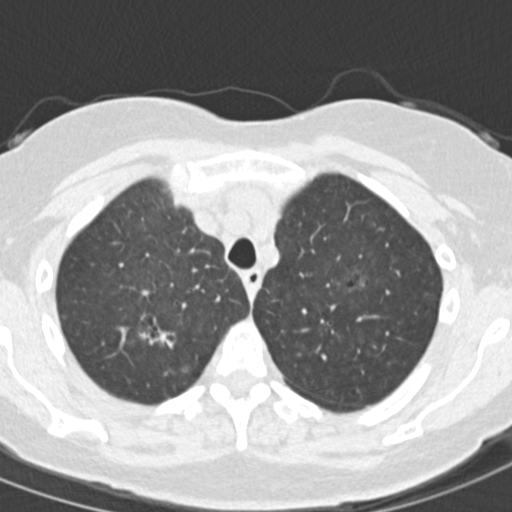
Low-dose screening chest CT, one axial slice. Slice 123 of 157 in the series (ordered by position). 120 kVp. Lung window (W 1500 / L -600 HU). 512 × 512 image matrix, field of view 280 × 280 mm.
Outlined on this slice (manually delineated by an expert):
- lesion 1 (tumor, upper lobe of right lung): box from (x=138, y=313) to (x=177, y=351) px